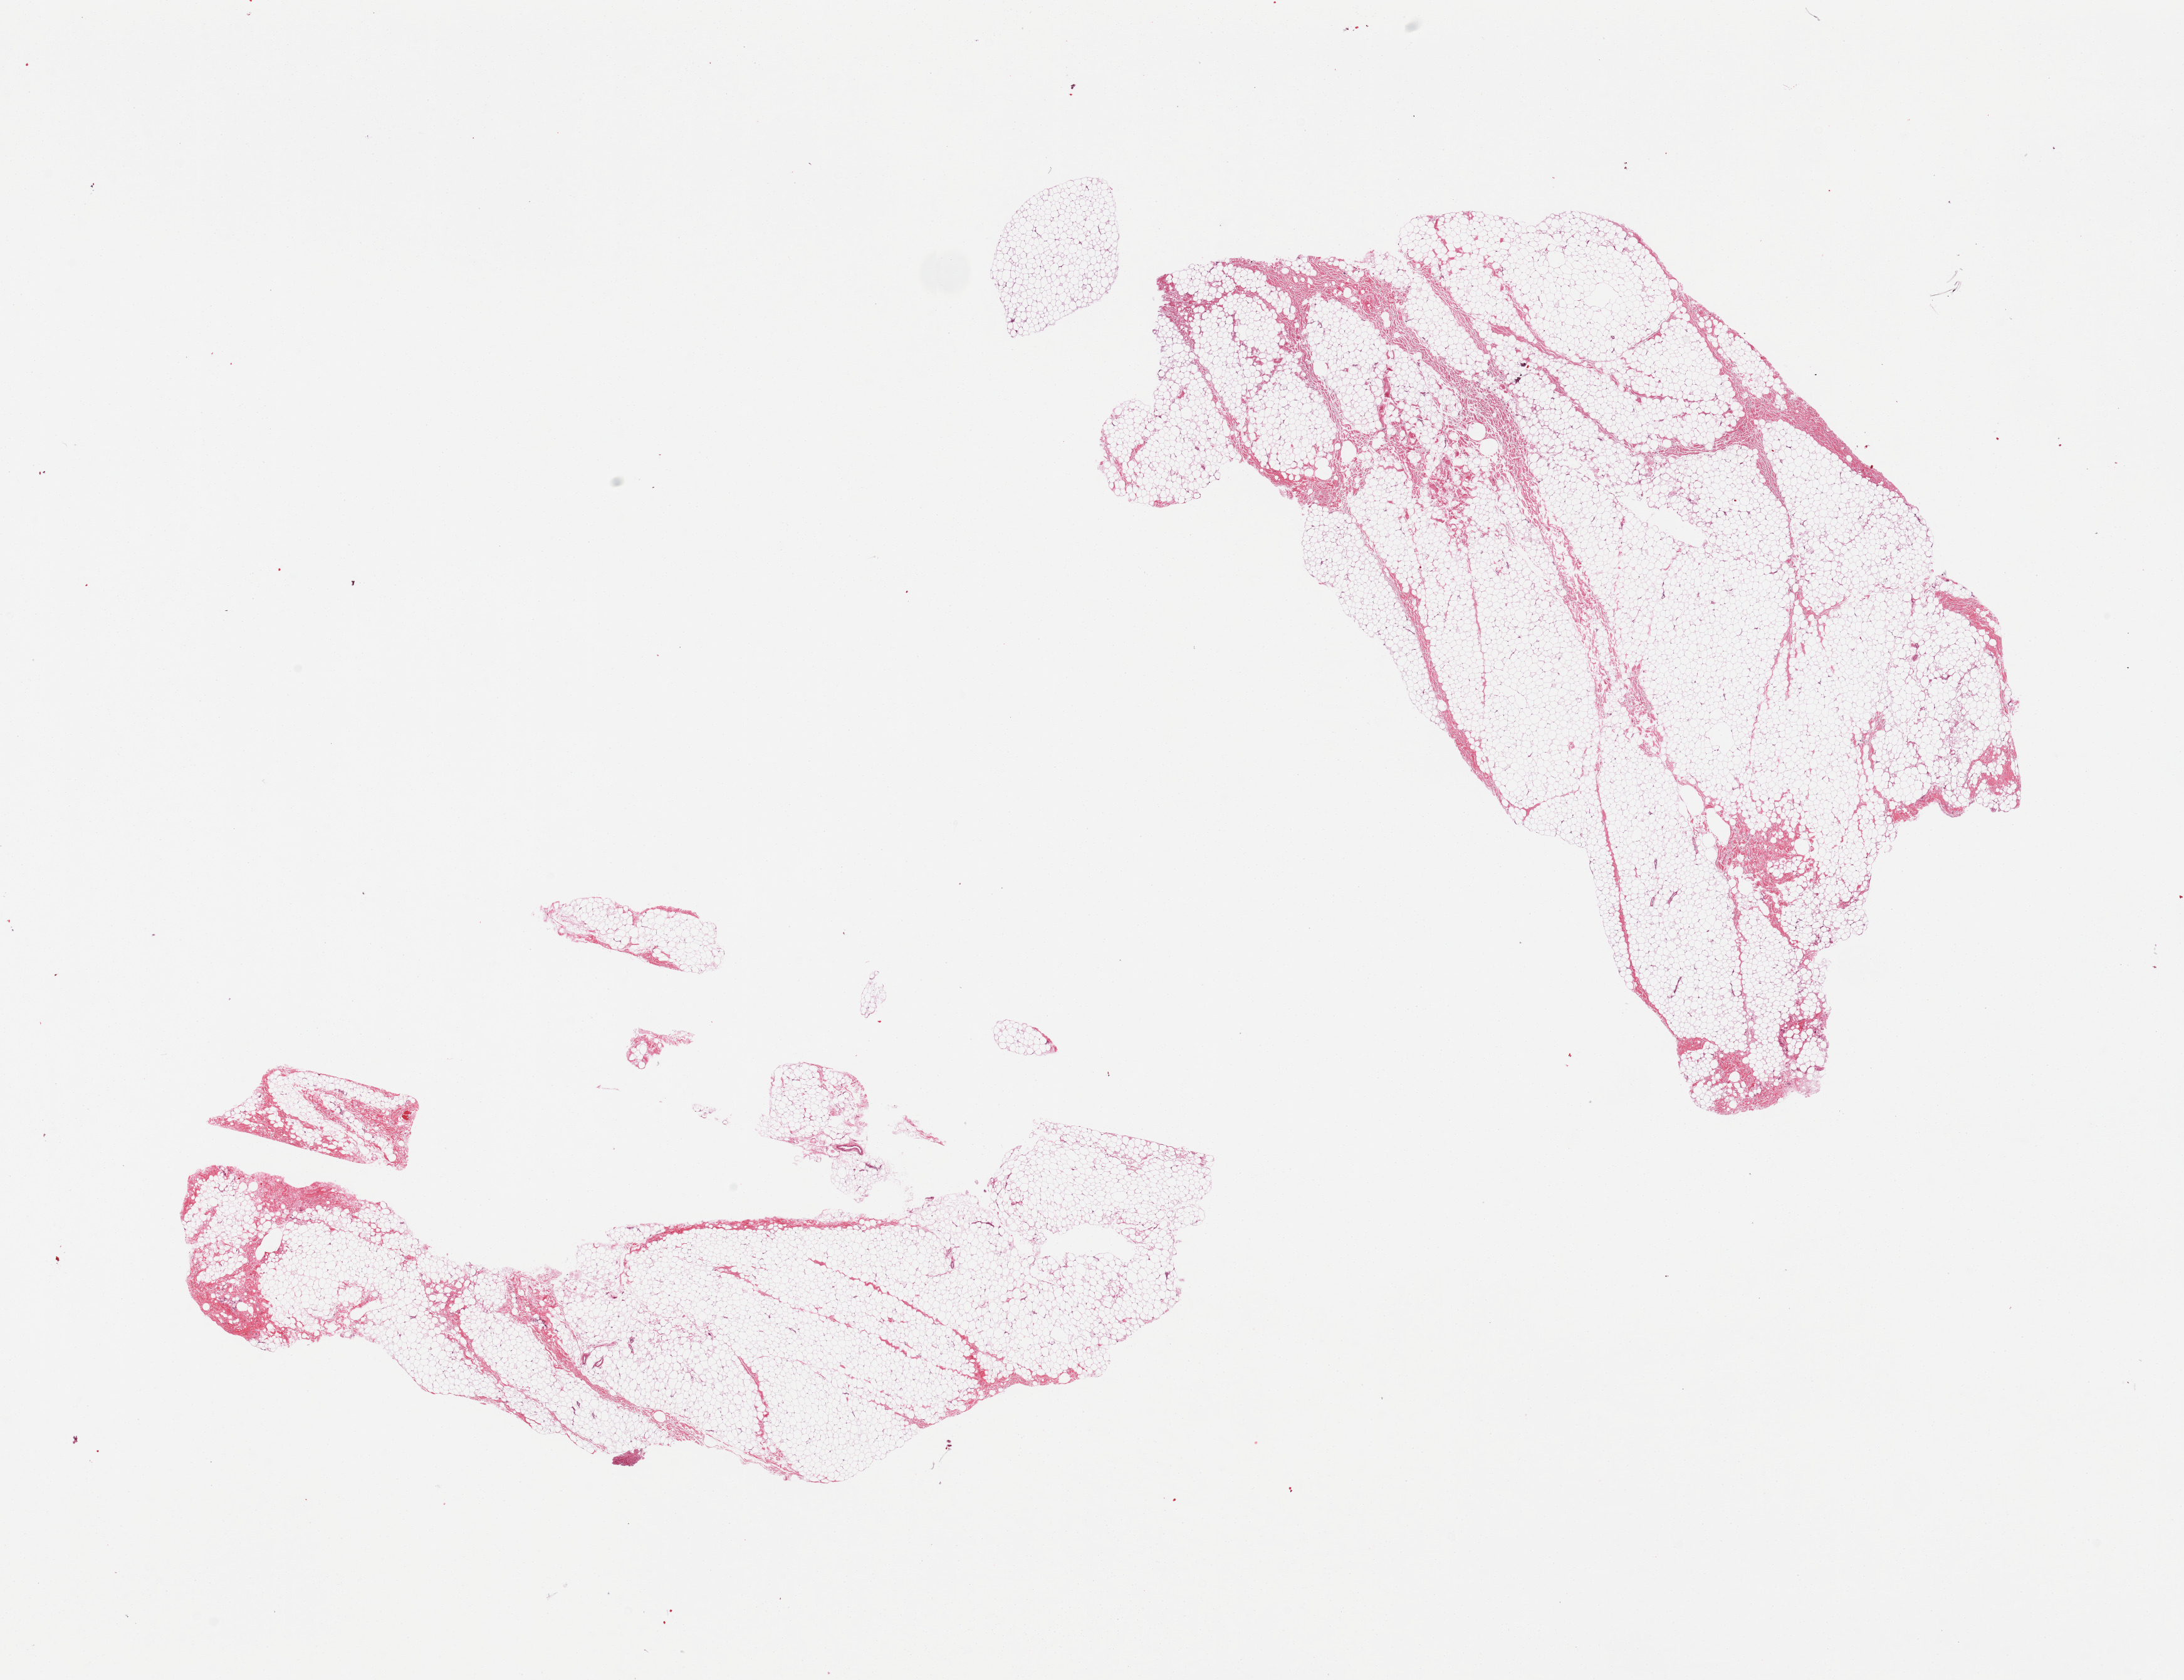
Hematoxylin and eosin (H&E) whole-slide image, a low-resolution overview of the entire scanned area, about 27.6 x 21.2 mm; PAXgene-fixed, paraffin-embedded tissue; target tissue: breast; donor tissue sample. Donor sex: male.
* reviewer comment on this tissue sample: 2 pieces, predominantly fat, ~5-10% fibrous, no ductal/lobular elements noted